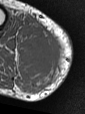
MRI of an extremity soft-tissue mass, one axial slice. Position 31 of 47 along the scan axis. MR volume resampled by the dataset authors to the PET/CT grid (not the native acquisition matrix). 3.27 mm slice thickness. 85 × 114 image matrix, field of view 83 × 111 mm. Male patient. From the clinical record (not read from this slice): histological type: pleiomorphic liposarcoma; grade: high; site of the primary tumour: right calf.
Outlined on this slice (expert contour drawn on MRI and transferred to this co-registered scan by the dataset authors):
- gross tumour volume including surrounding oedema: bounding box (x1, y1, x2, y2) in pixels: (20, 27, 64, 76)
- gross tumour volume (mass): (29, 35, 64, 70)